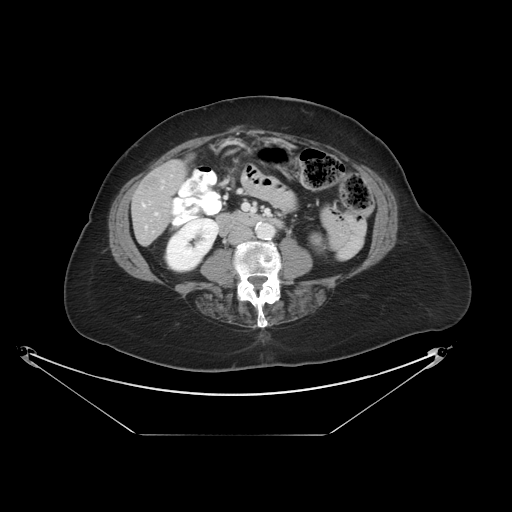
Contrast-enhanced abdominal CT, one axial slice; position 7 of 36 along the scan axis; reconstruction kernel STANDARD; intravenous contrast given; soft-tissue window (W 400 / L 40 HU); 5 mm slice thickness; 512 × 512 image matrix, field of view 500 × 500 mm. Female patient, age 70 years. From the clinical record (not read from this slice): diagnosis: colorectal cancer liver metastases, imaged before liver resection; multiple liver metastases: no; largest metastasis: 2.5 cm; disease in both lobes: no.
Outlined on this slice (expert manual segmentation):
- hepatic veins: bounding box (x1, y1, x2, y2) in pixels: (143, 205, 145, 207)
- liver: (133, 161, 185, 244)